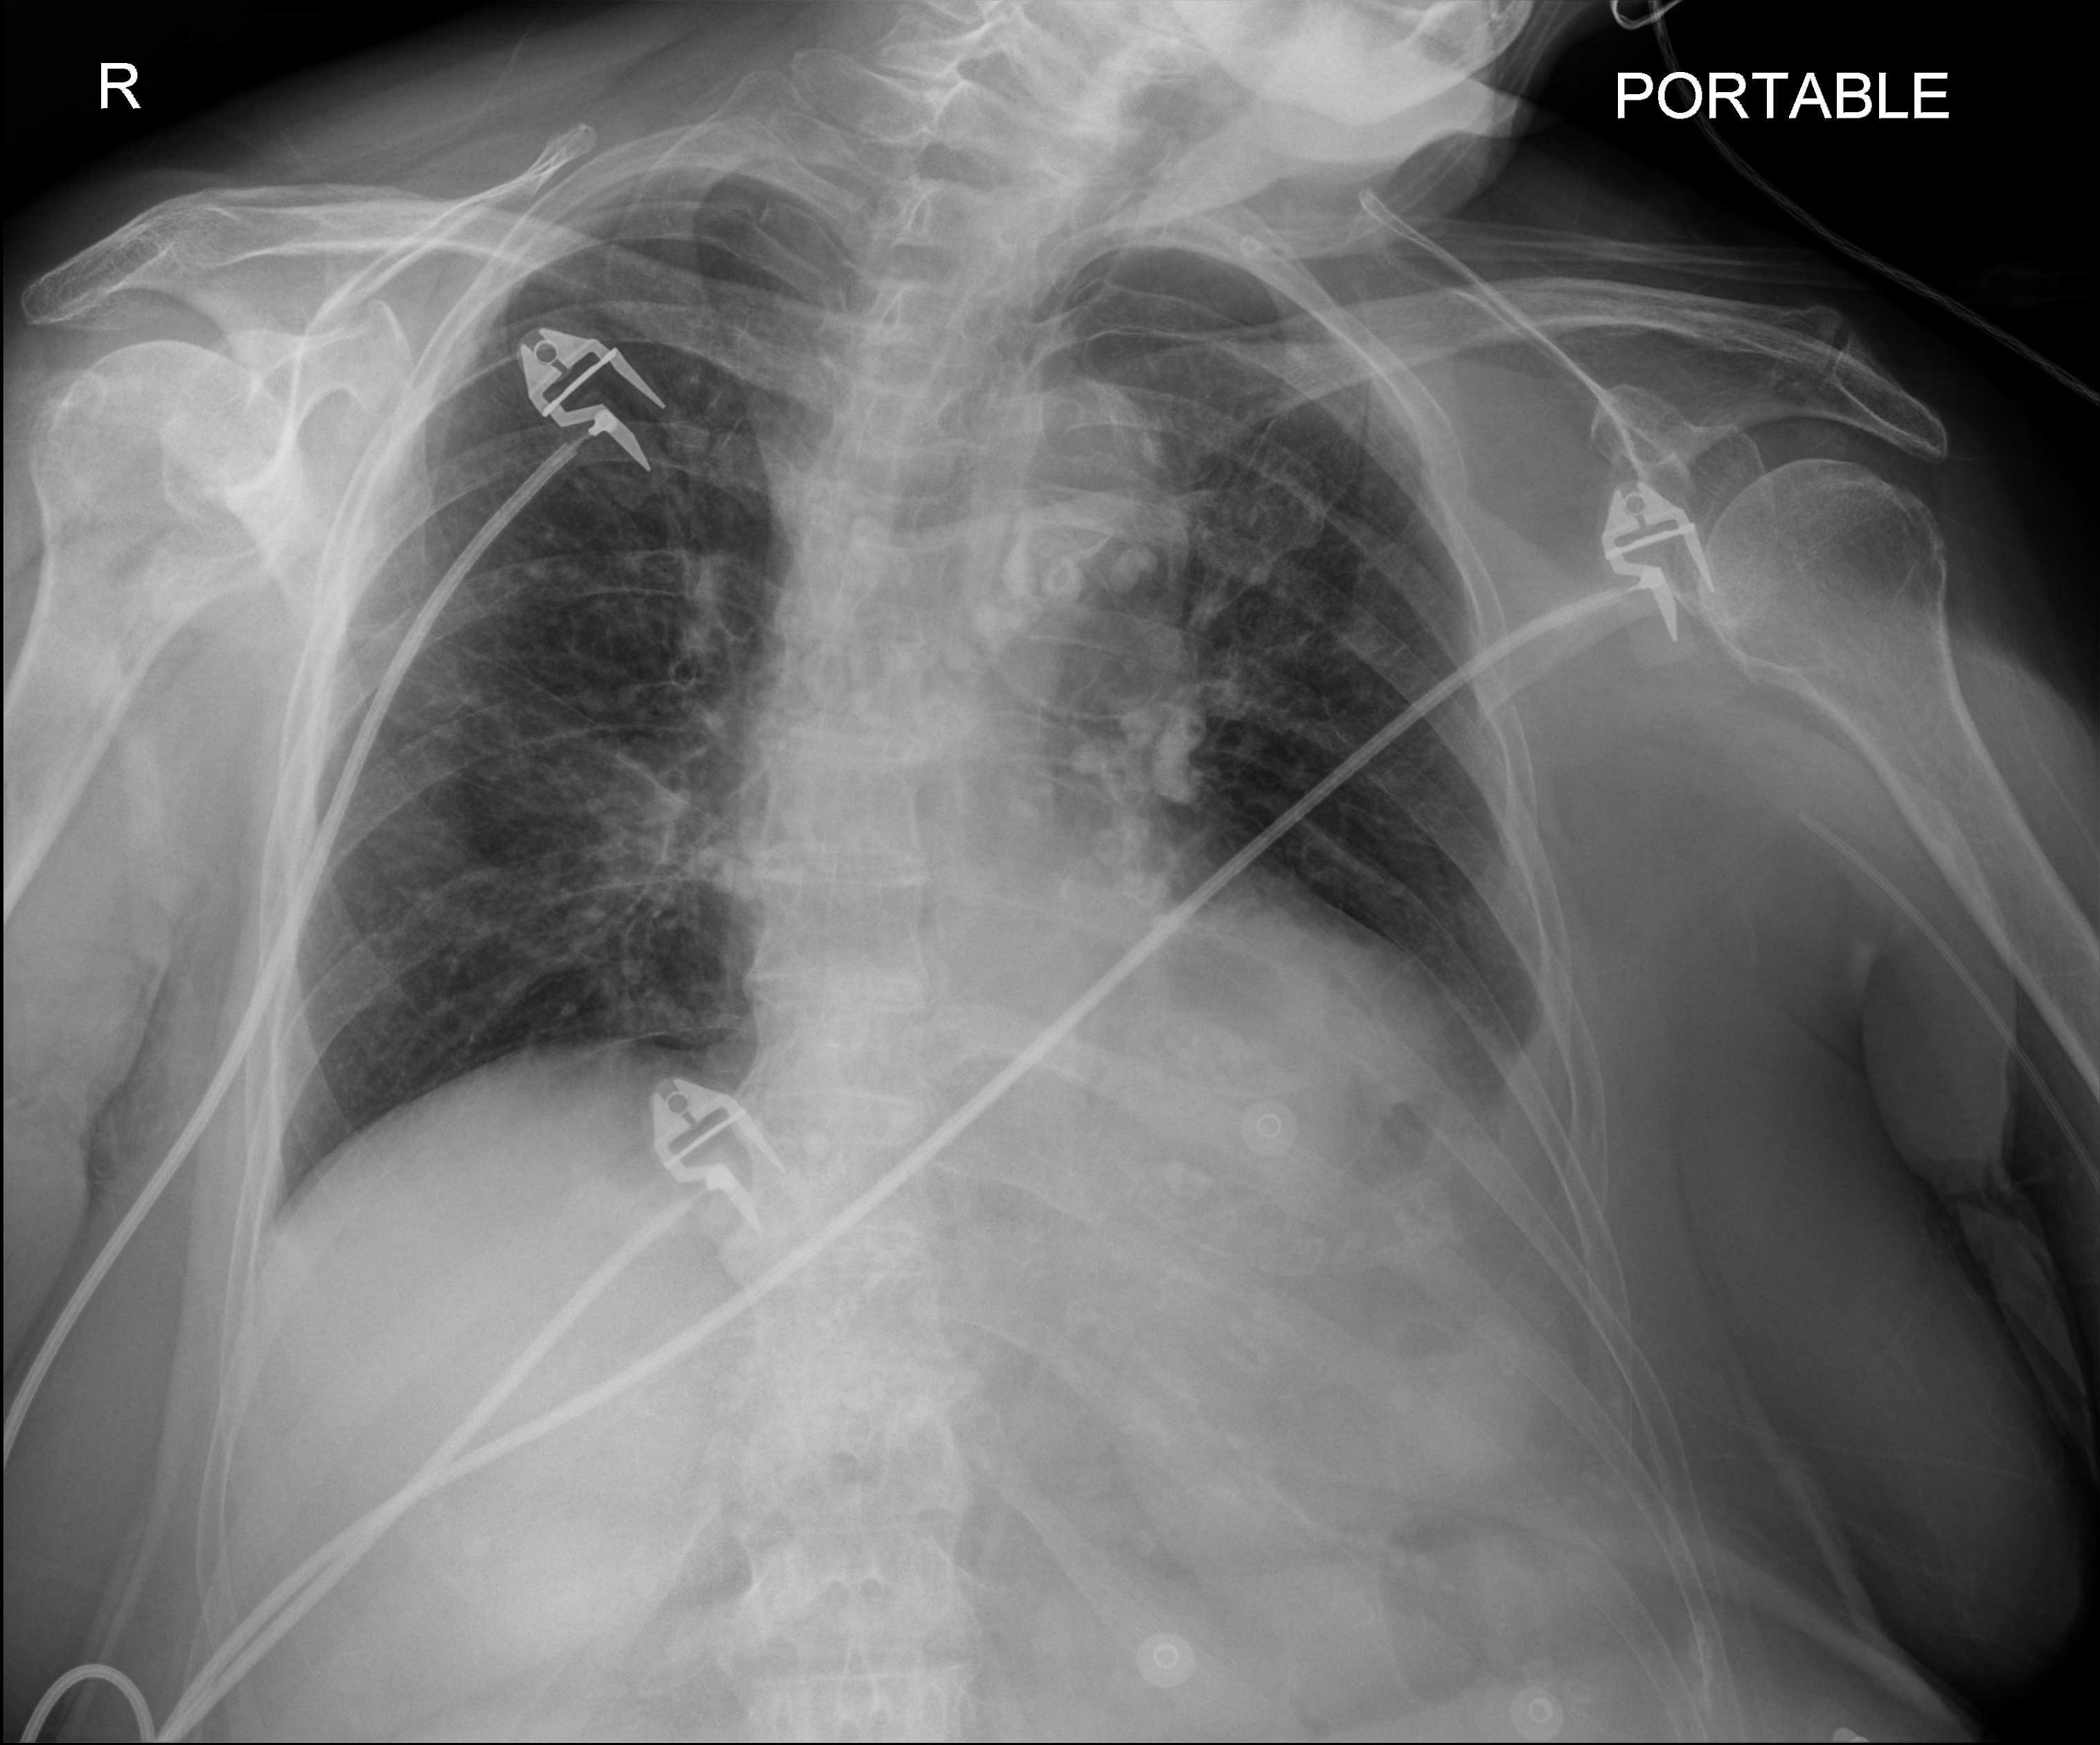
Portable chest radiograph; anteroposterior (AP) projection. Female patient hospitalised with COVID-19, age 75–90 years.
Admission-level facts for this patient (not findings on this image; timing relative to this image not recorded):
- admitted to intensive care during this hospital stay: no
- mechanically ventilated during this hospital stay: no